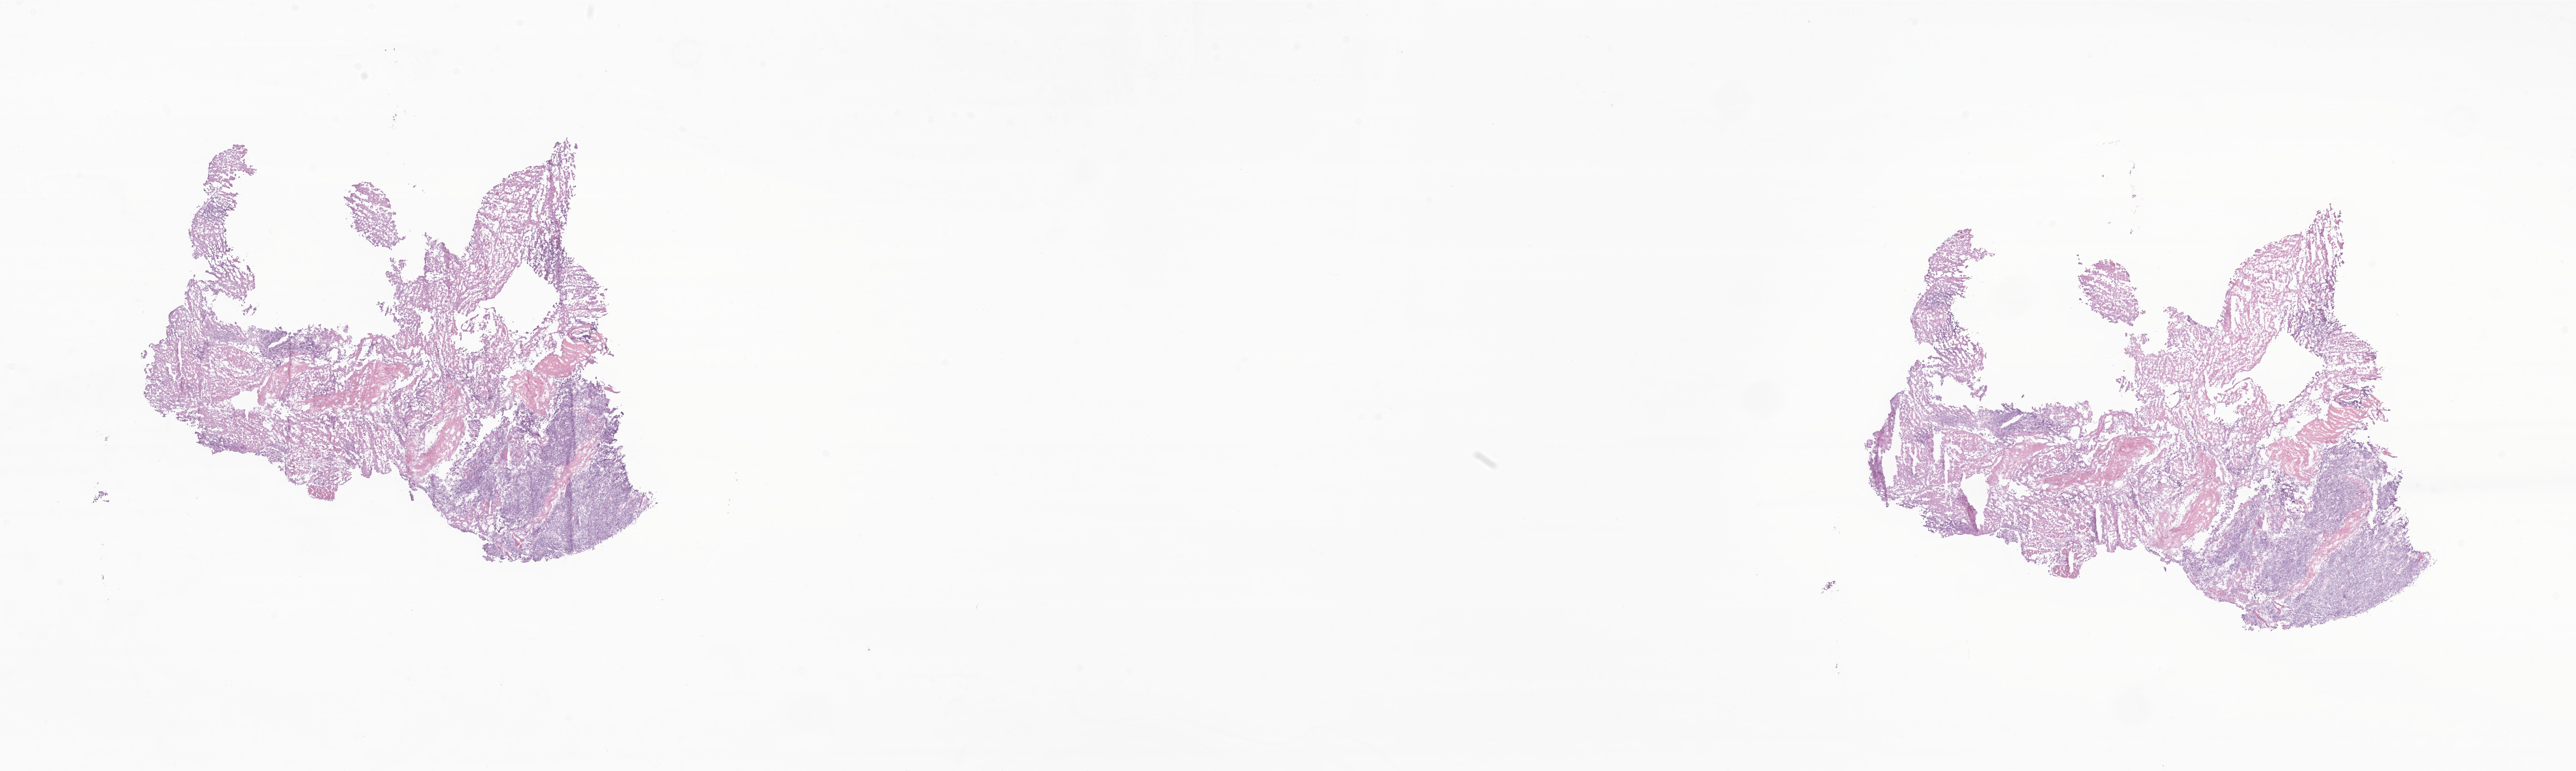
Whole-slide image, haematoxylin and eosin stain of tumor tissue from the spinal cord, shown as a low-resolution overview of the whole scanned area (about 33.5 x 10.0 mm), cryosection (OCT / tissue freezing medium). Patient female; age 142 months (11 years 10 months).
Recorded diagnosis: Undifferentiated sarcoma.